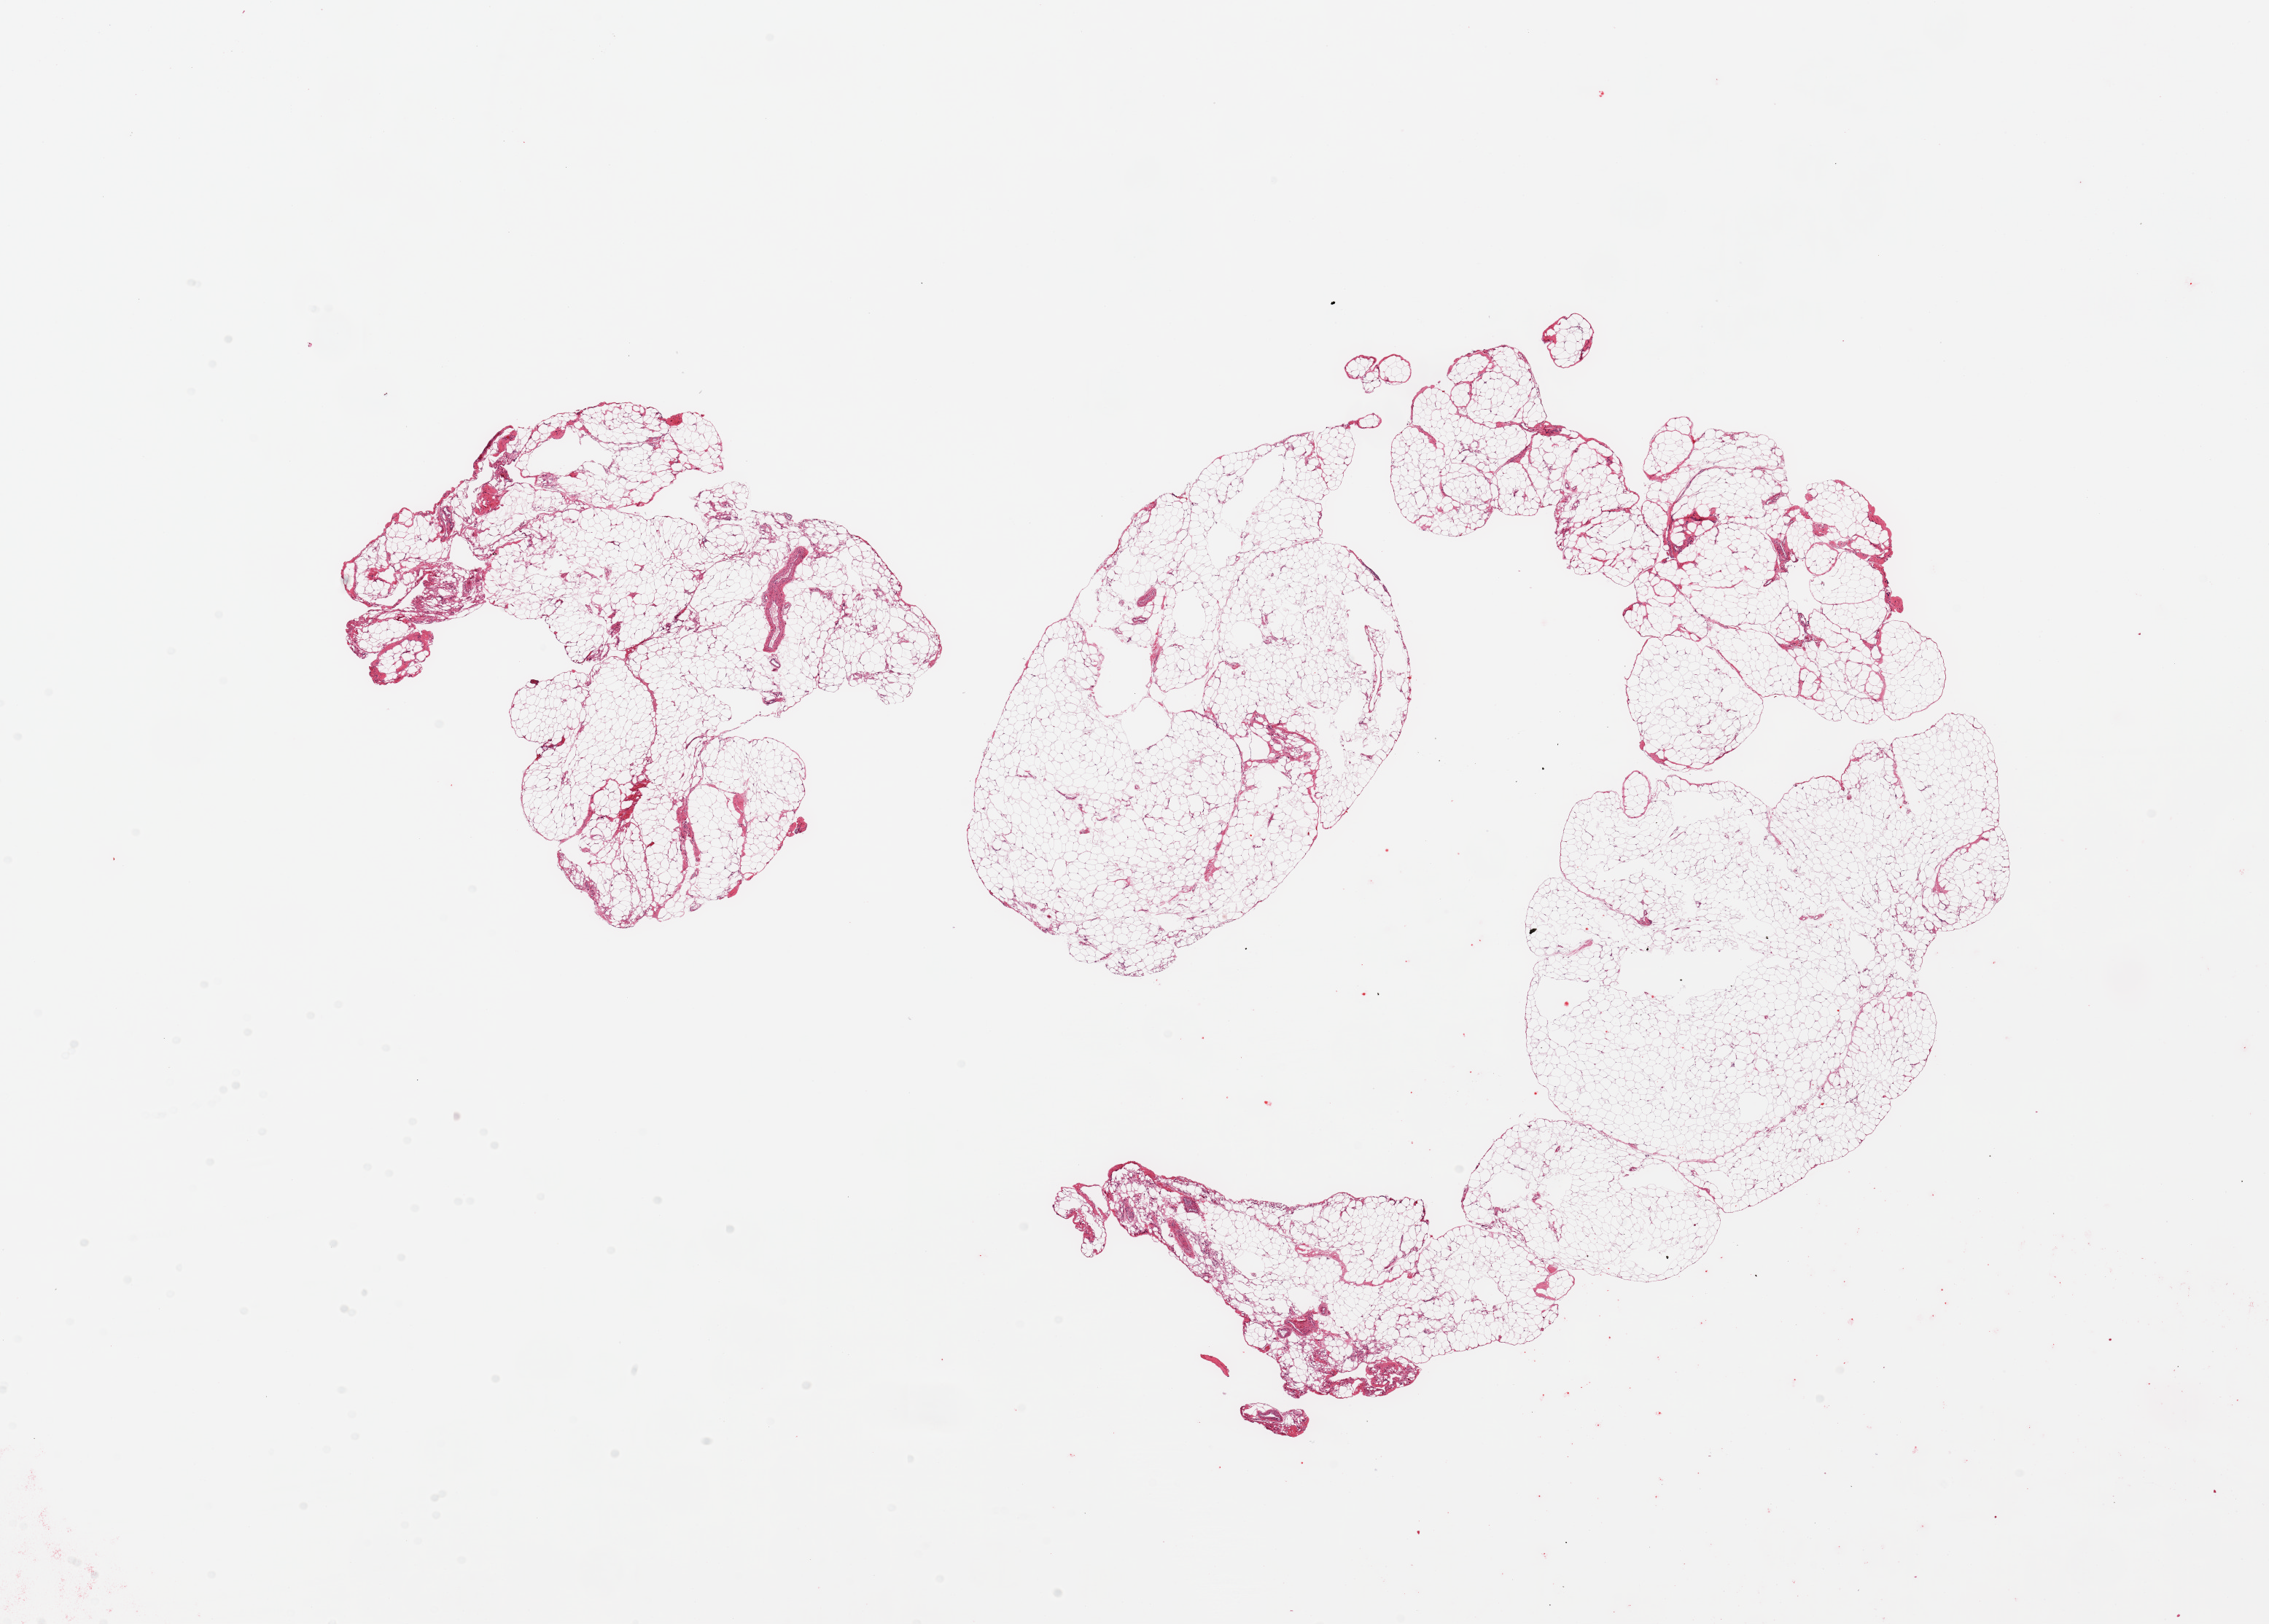
Haematoxylin and eosin whole-slide image — a low-resolution overview of the entire scanned area, about 24.6 x 17.6 mm. PAXgene-fixed, paraffin-embedded tissue. Section of omentum (target tissue). Tissue donor sample.
Review note (as recorded): 2 pieces, 5-10% fascia/vascular elements.